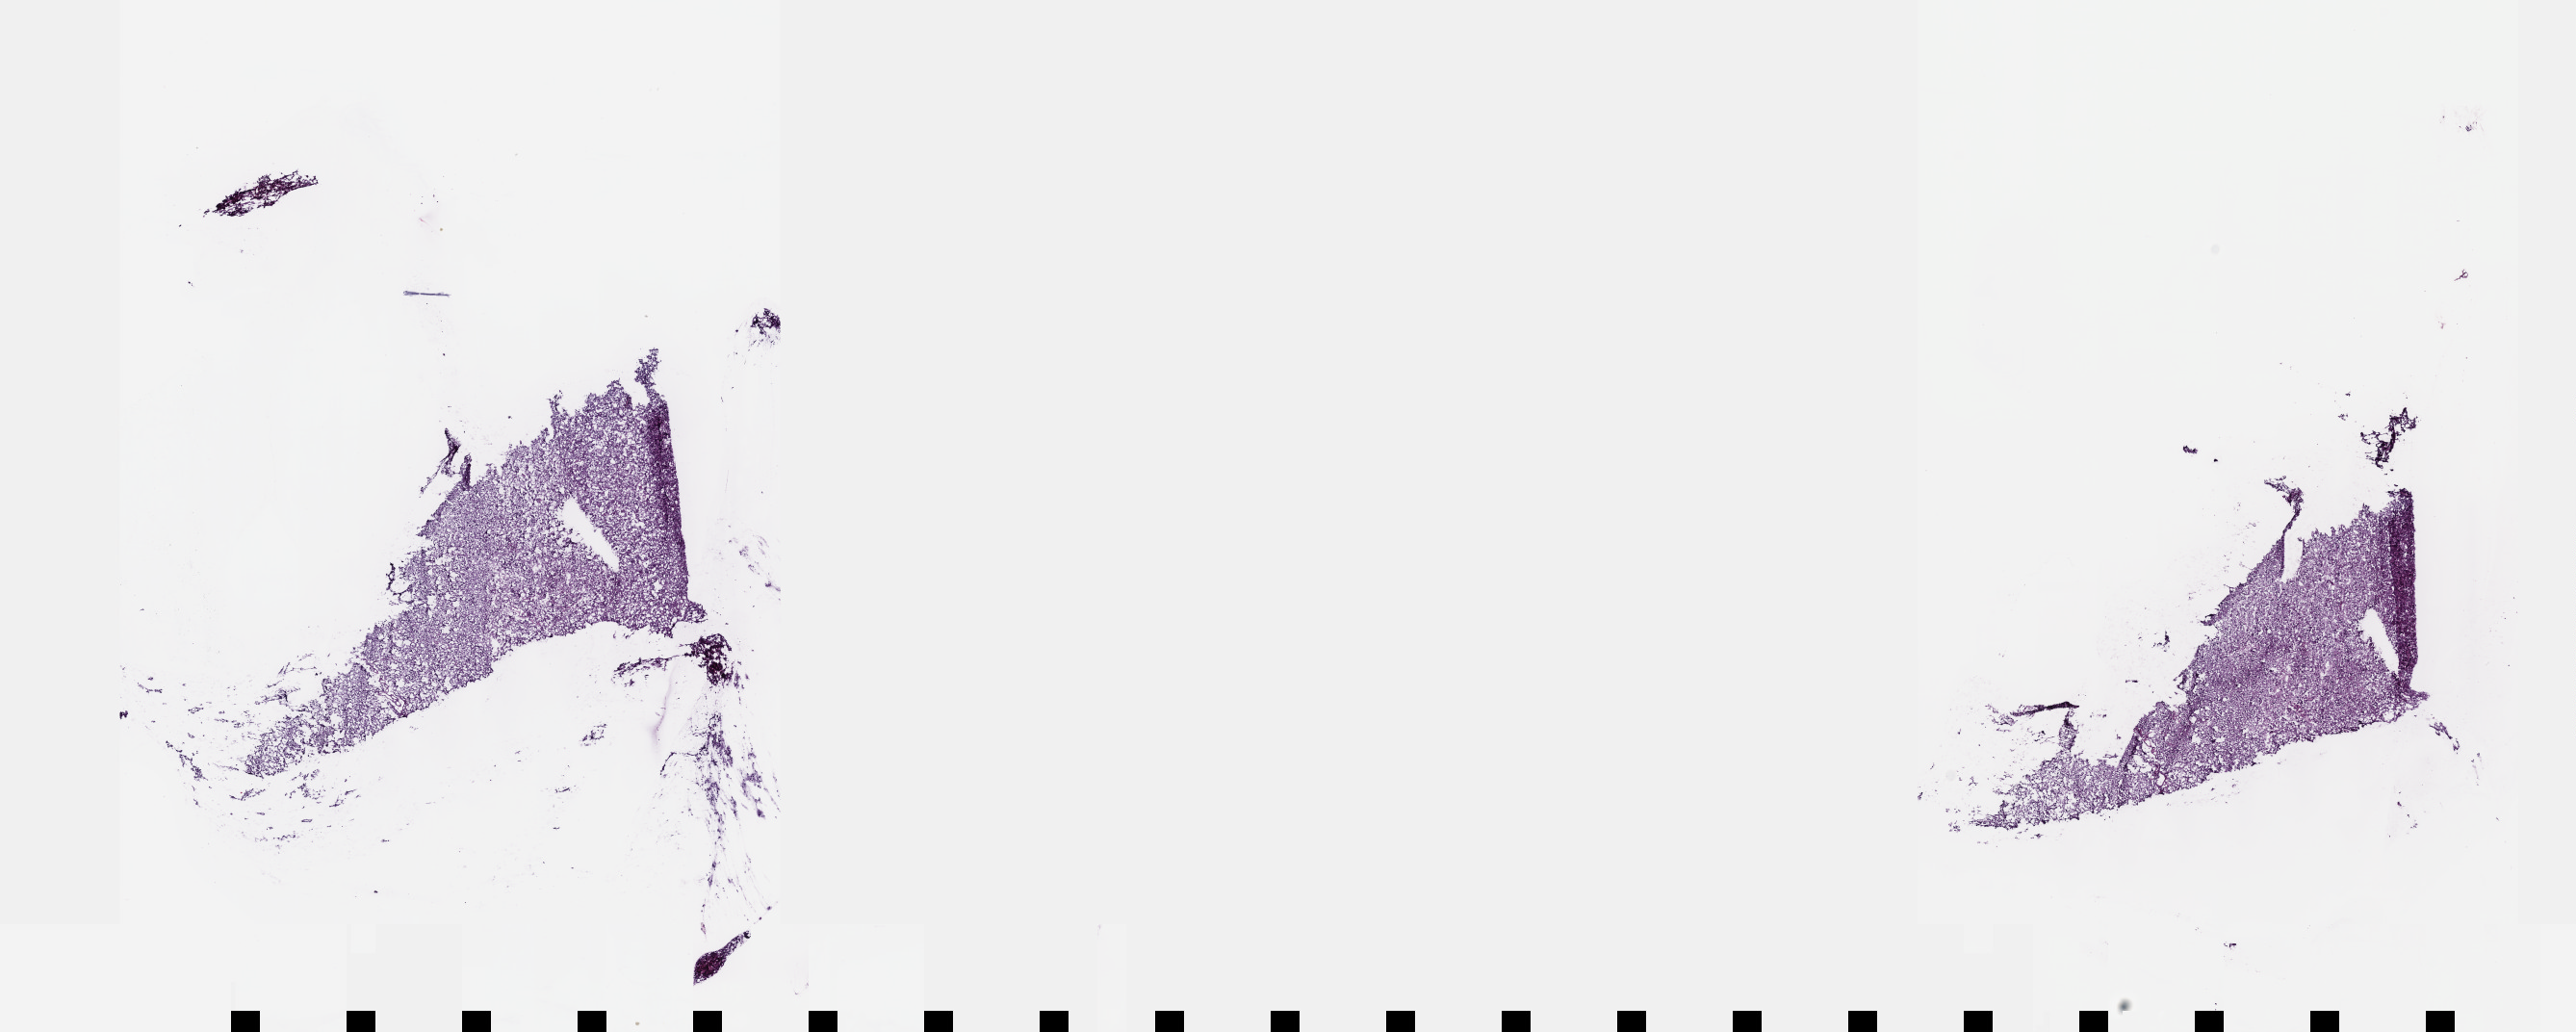
Digitized Hematoxylin and eosin (H&E) stained tissue section (whole slide) — low-resolution overview of the scanned area, about 21.6 x 8.7 mm; frozen section; sample: primary tumour, brain. Male patient; age at initial diagnosis 45 years. Histologic grade: G3 (poorly differentiated). Pathologist review of this section (percent, as recorded): tumour cells 65%, tumour nuclei 90%, normal cells 10%, stromal cells 25%, necrosis 0%. Inflammatory infiltration, as recorded: lymphocyte infiltration 0%, monocyte infiltration 0%, neutrophil infiltration 0%.
• pathologic diagnosis: Oligodendroglioma, anaplastic (cerebrum)